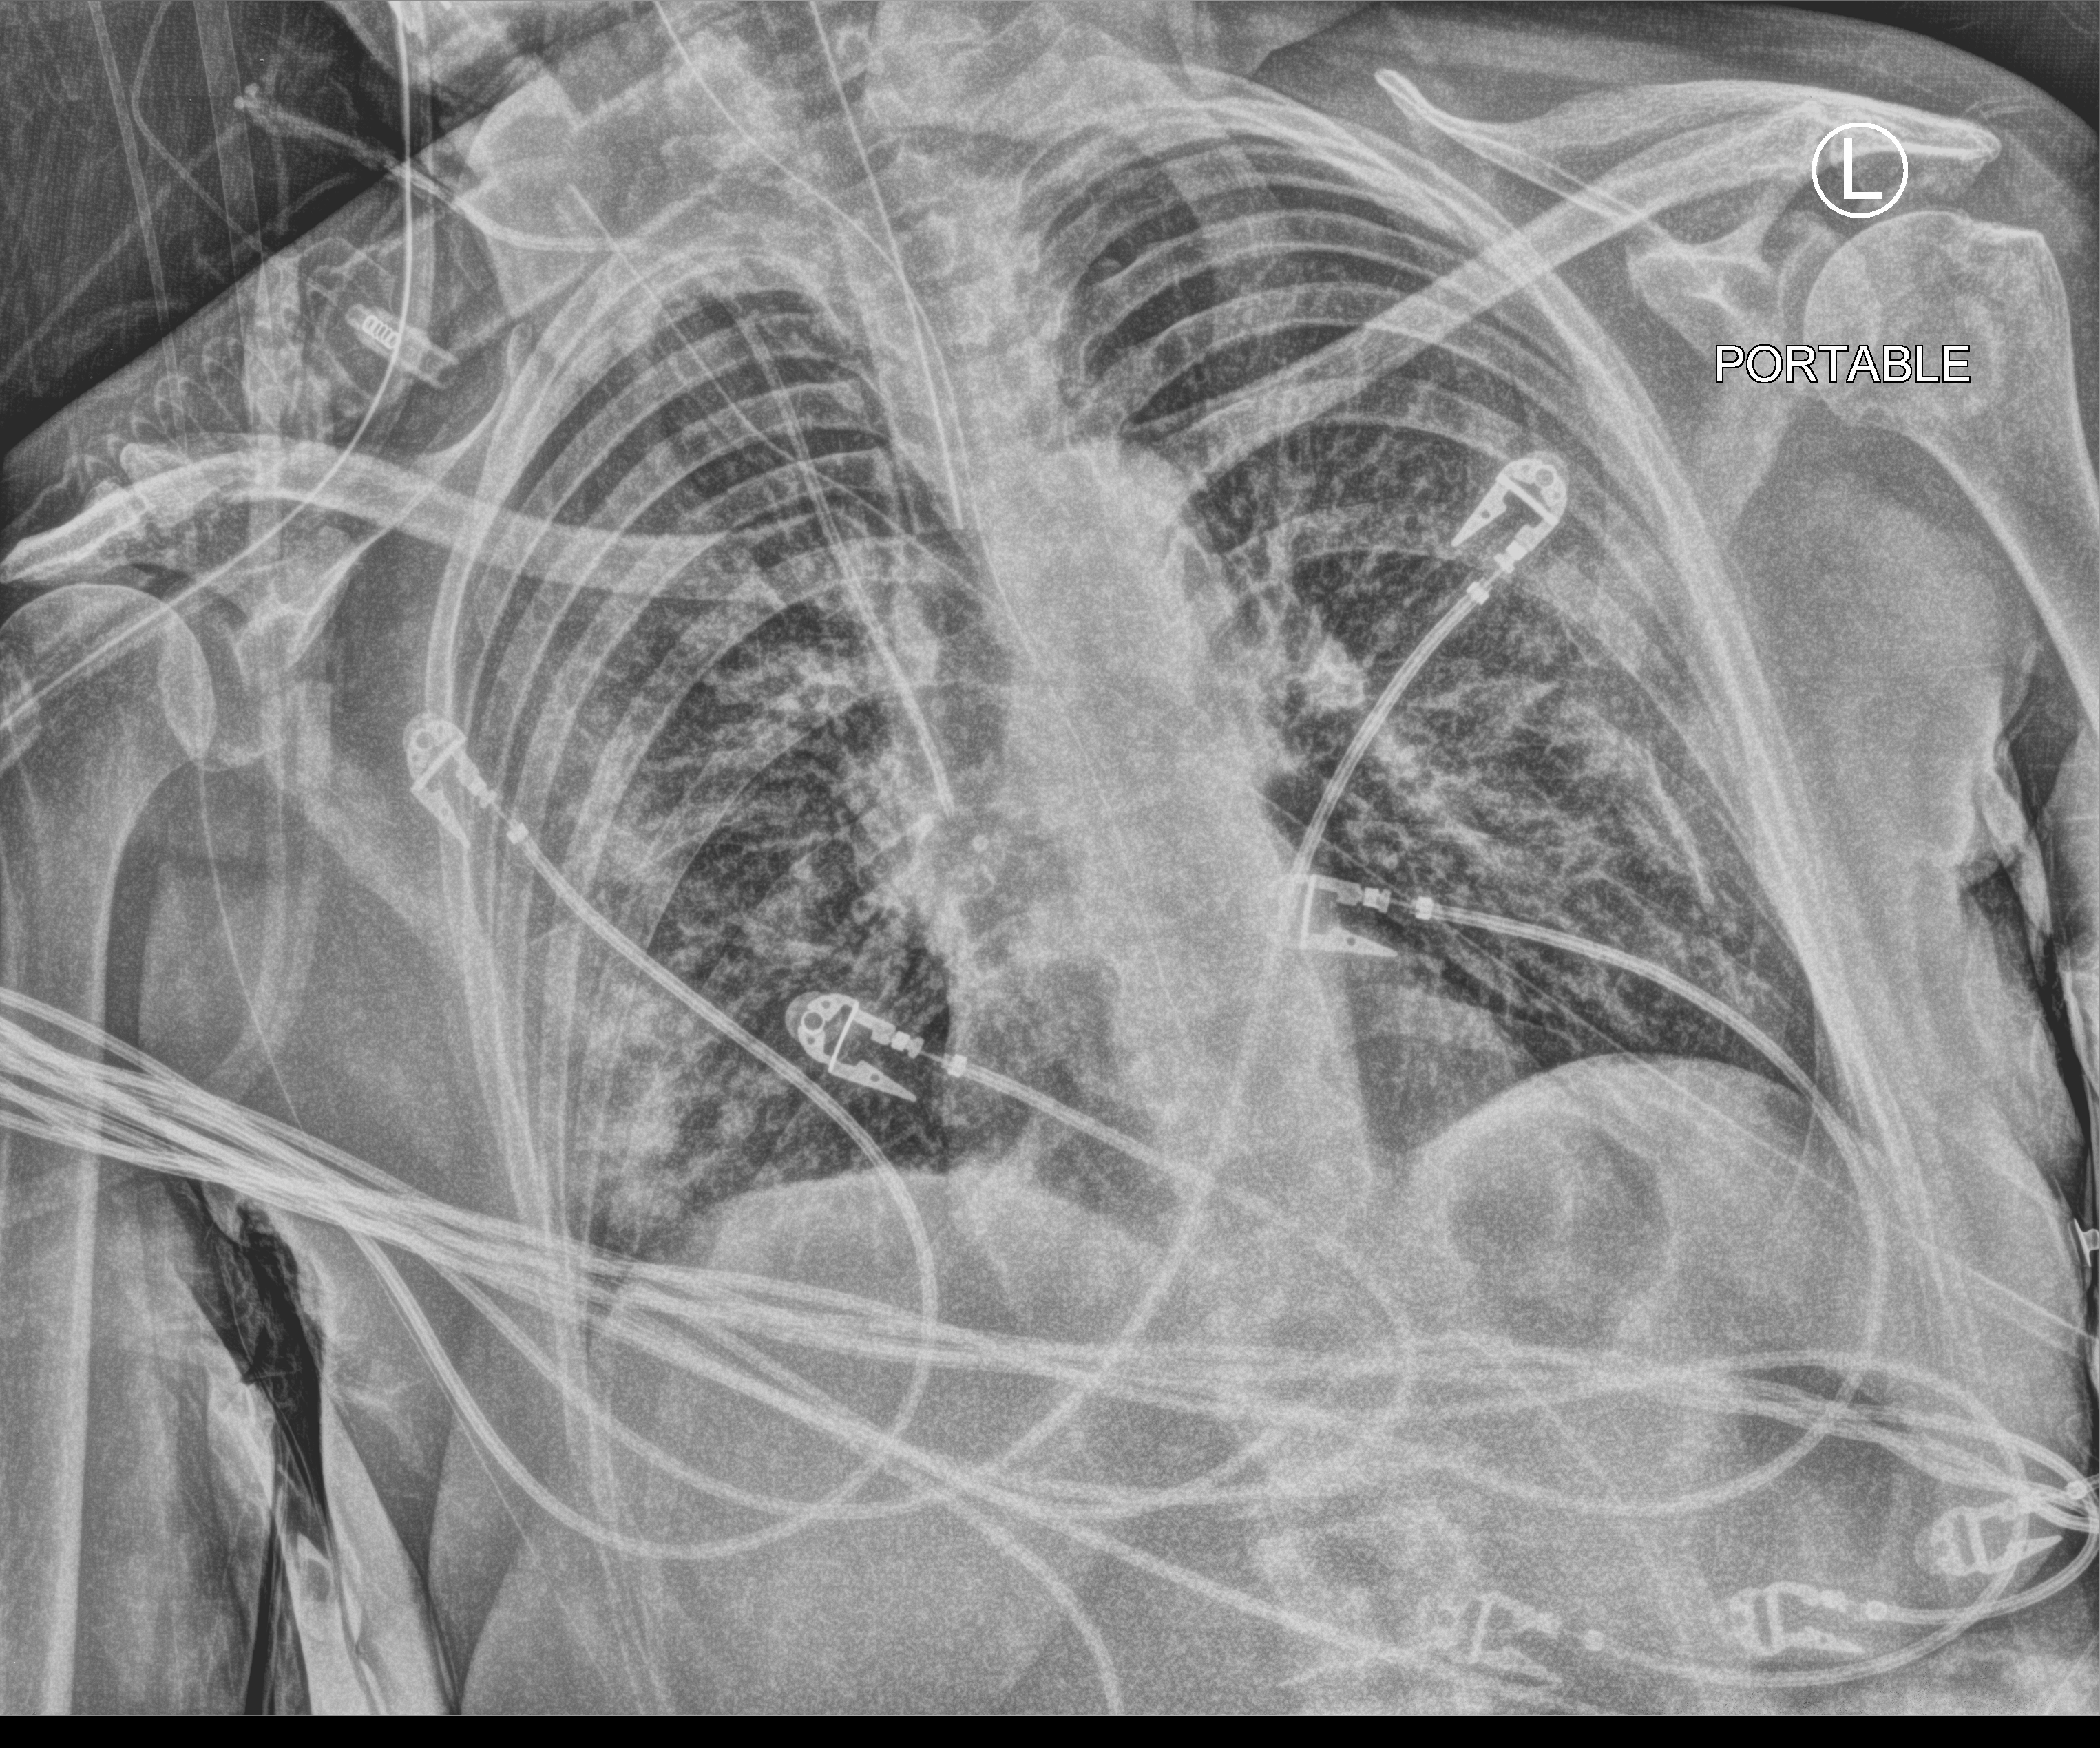
Portable chest radiograph, anteroposterior (AP) projection. Patient hospitalised with COVID-19; female, aged 60–74 years.
From the hospital-stay record, not from the radiograph (when in the stay this image was taken is not recorded): admitted to intensive care during this hospital stay: yes.